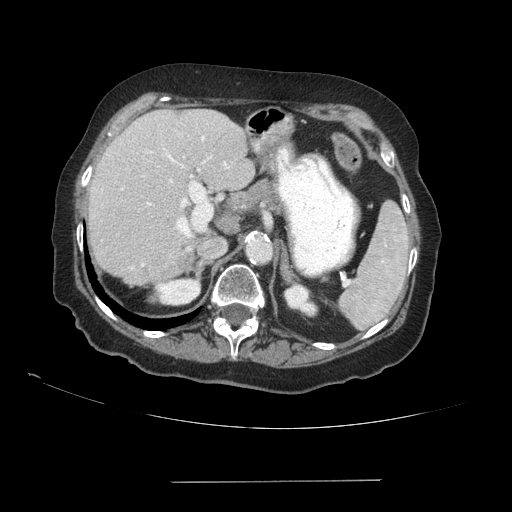
Contrast-enhanced abdominal CT (liver protocol), one axial slice; slice 60 of 89 in the series (ordered by position); 140 kVp; soft-tissue window (W 400 / L 40 HU); 512 × 512 image matrix, field of view 400 × 400 mm. From the clinical record (not read from this slice): diagnosis: hepatocellular carcinoma (patient treated with transarterial chemoembolisation; whether this scan precedes or follows treatment is not stated here); TNM stage (as recorded): Stage-IVA; Child-Pugh class: A; tumour nodularity: uninodular.
Outlined on this slice (semi-automatically segmented with operator editing):
- liver parenchyma outside the tumour (the mass and vessels are separate outlines, so this box may not span the whole liver): bounding box (x1, y1, x2, y2) in pixels: (88, 110, 254, 286)
- liver vessels: (121, 136, 228, 267)